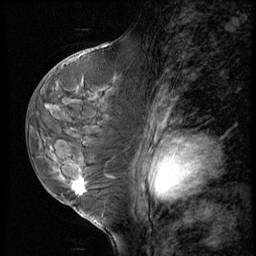
Breast MRI (dynamic contrast-enhanced), one sagittal slice. Slice 33 of 60 in the series (ordered by position). 3 images stored at this slice position (order not interpretable as contrast timing). 1.5 T. TE 4.2 ms, TR 8.9 ms. 2.5 mm slice thickness. 256 × 256 image matrix. Patient: female, 50 years. From the clinical record (not read from this slice): setting: breast cancer imaged before/during neoadjuvant chemotherapy; receptor status: HR-positive, HER2-negative.
Outlined on this slice (semi-automatic segmentation, software-assisted and operator-edited):
- analysis volume of interest (the breast-tissue region the enhancement analysis was run in; not a lesion): box from (x=38, y=102) to (x=118, y=213) px
- tumour enhancement mask (voxels above the 140 % enhancement threshold inside the analysis volume of interest): (x=72, y=180)–(x=87, y=195)